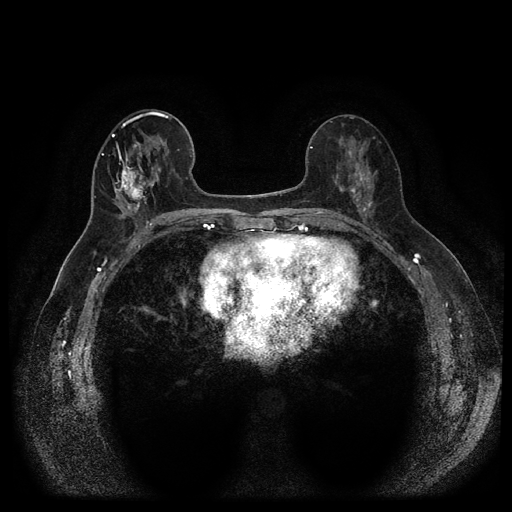
Breast MRI (dynamic contrast-enhanced, multi-phase), one axial slice. Position 45 of 116 along the scan axis. Dynamic contrast-enhanced series, time point 2 of 5 at this slice position (early post-contrast). 1.5 T. TE 2.6 ms, TR 5.4 ms. 2 mm slice thickness. 512 × 512 image matrix, field of view 340 × 340 mm. Female patient, age 56 years.
Outlined on this slice (semi-automatic segmentation, software-assisted and operator-edited):
- breast lesion (labelled 'tumour' in the annotation; benign lesions carry a separate 'benign' label): box from (x=112, y=162) to (x=150, y=213) px